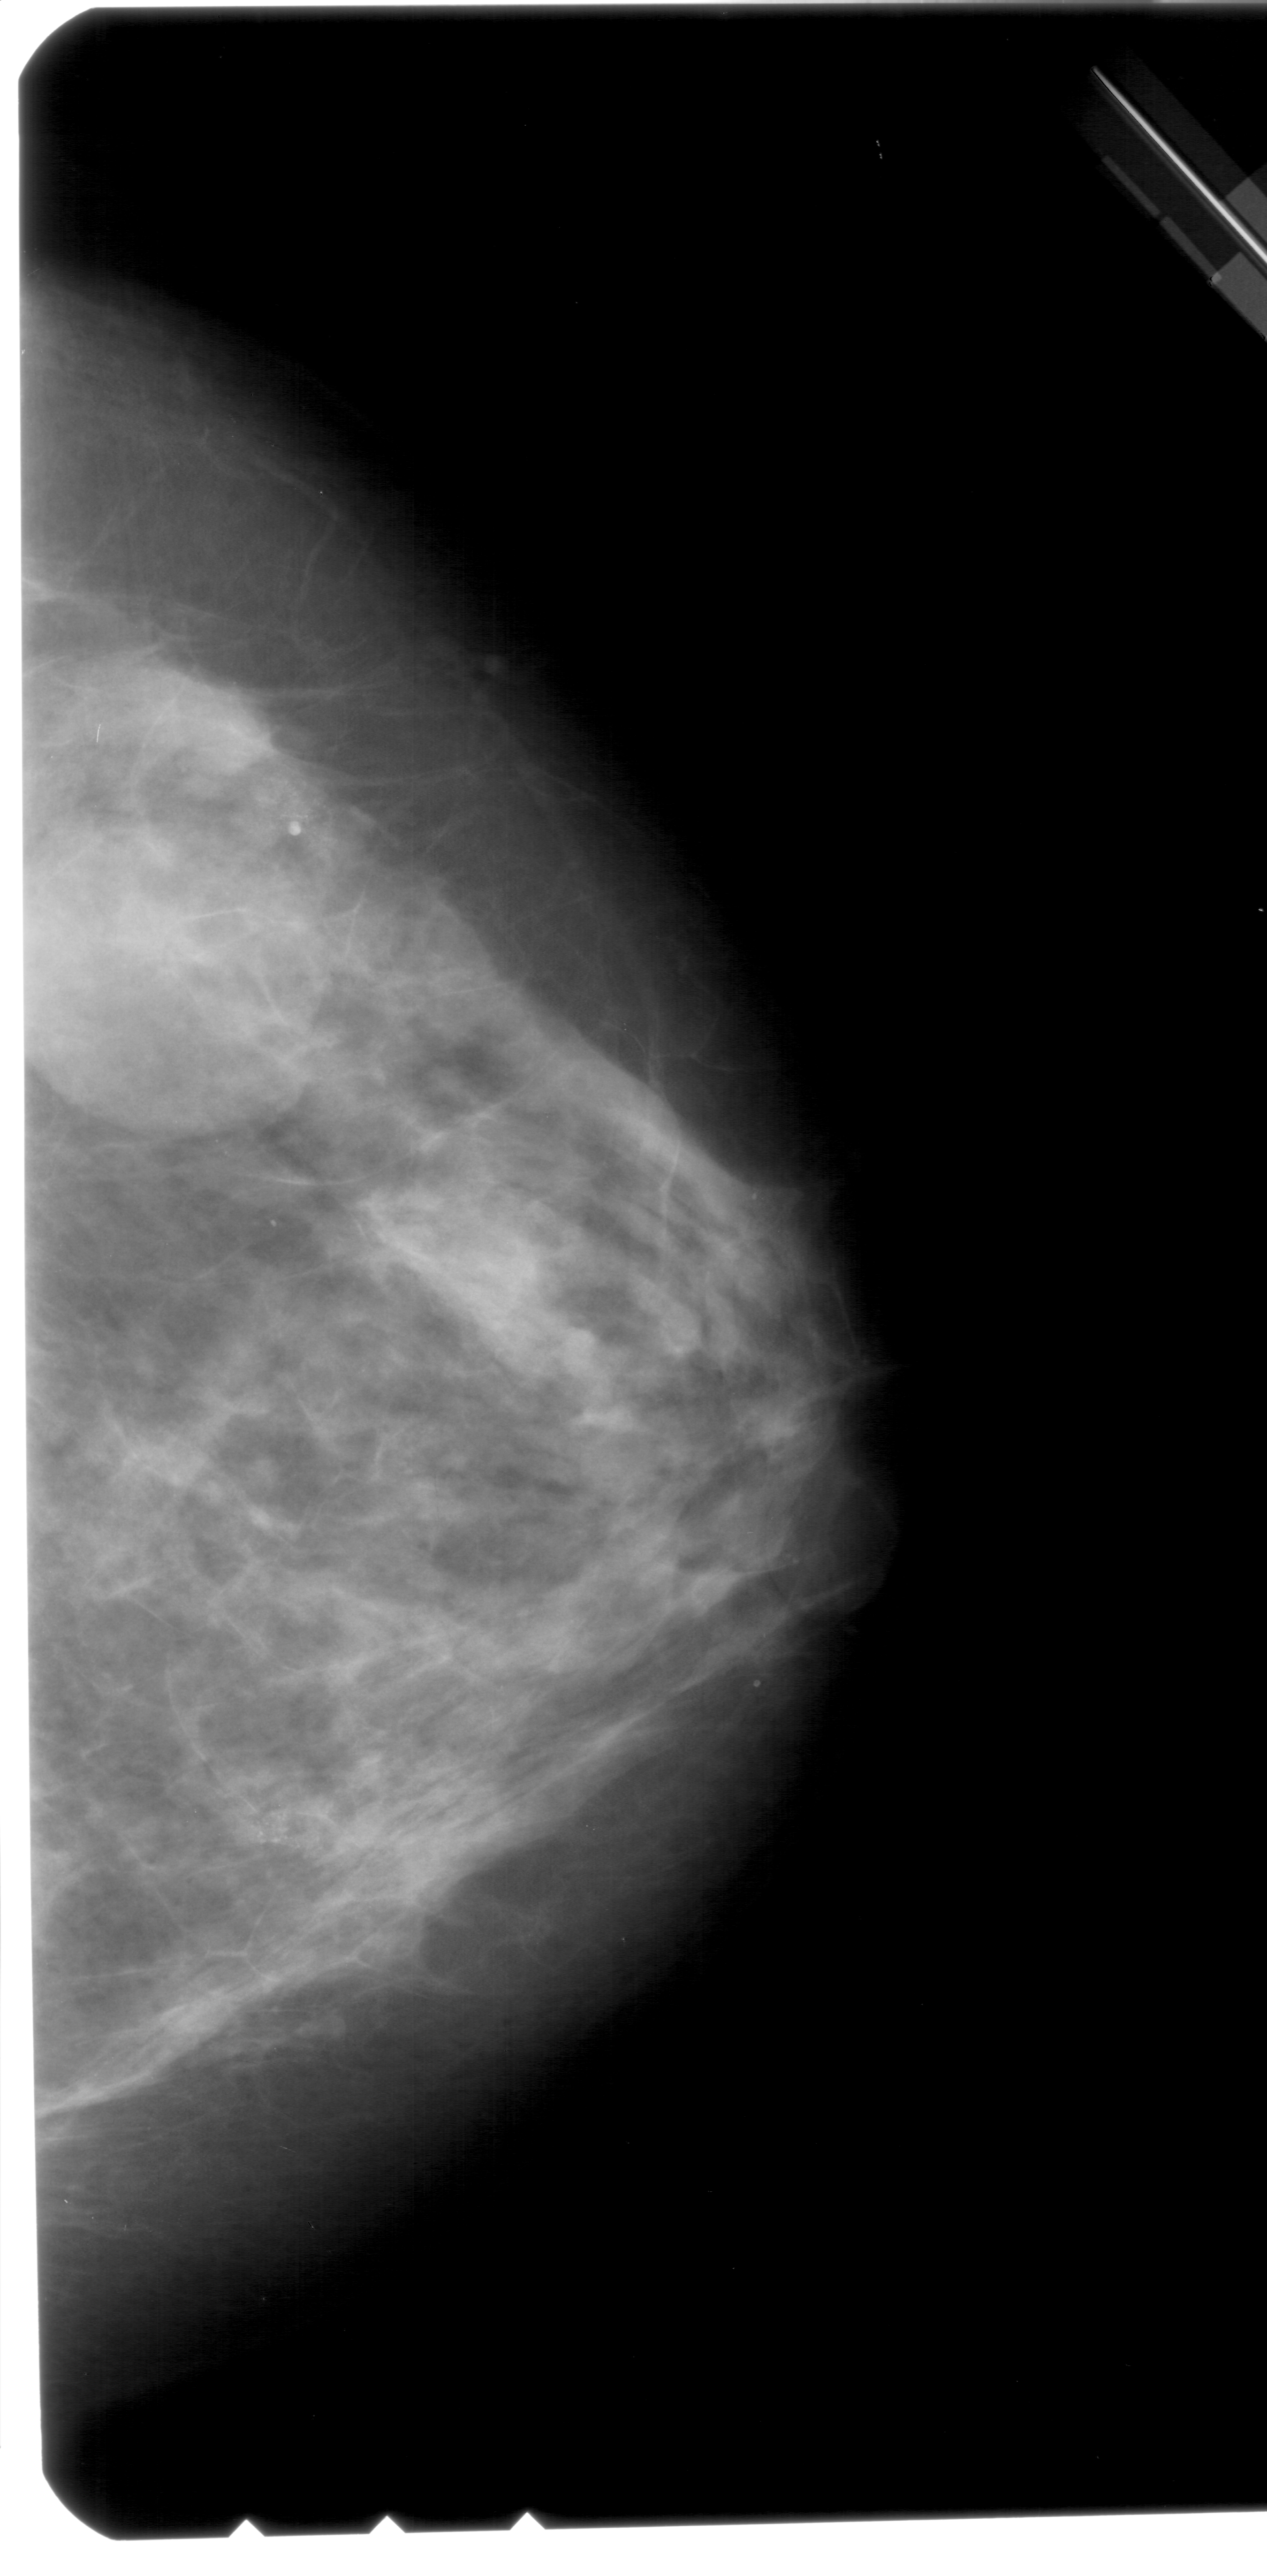
Scanned film-screen mammogram; right breast; craniocaudal (CC) view; BI-RADS breast density category 3 (scale 1–4); 1267 × 2576 image matrix.
Marked abnormalities (boxes around the expert regions of interest):
- calcifications, morphology pleomorphic, distribution clustered; BI-RADS assessment category 4; pathology (as recorded): benign: bounding box (x1, y1, x2, y2) in pixels: (242, 771, 356, 866)